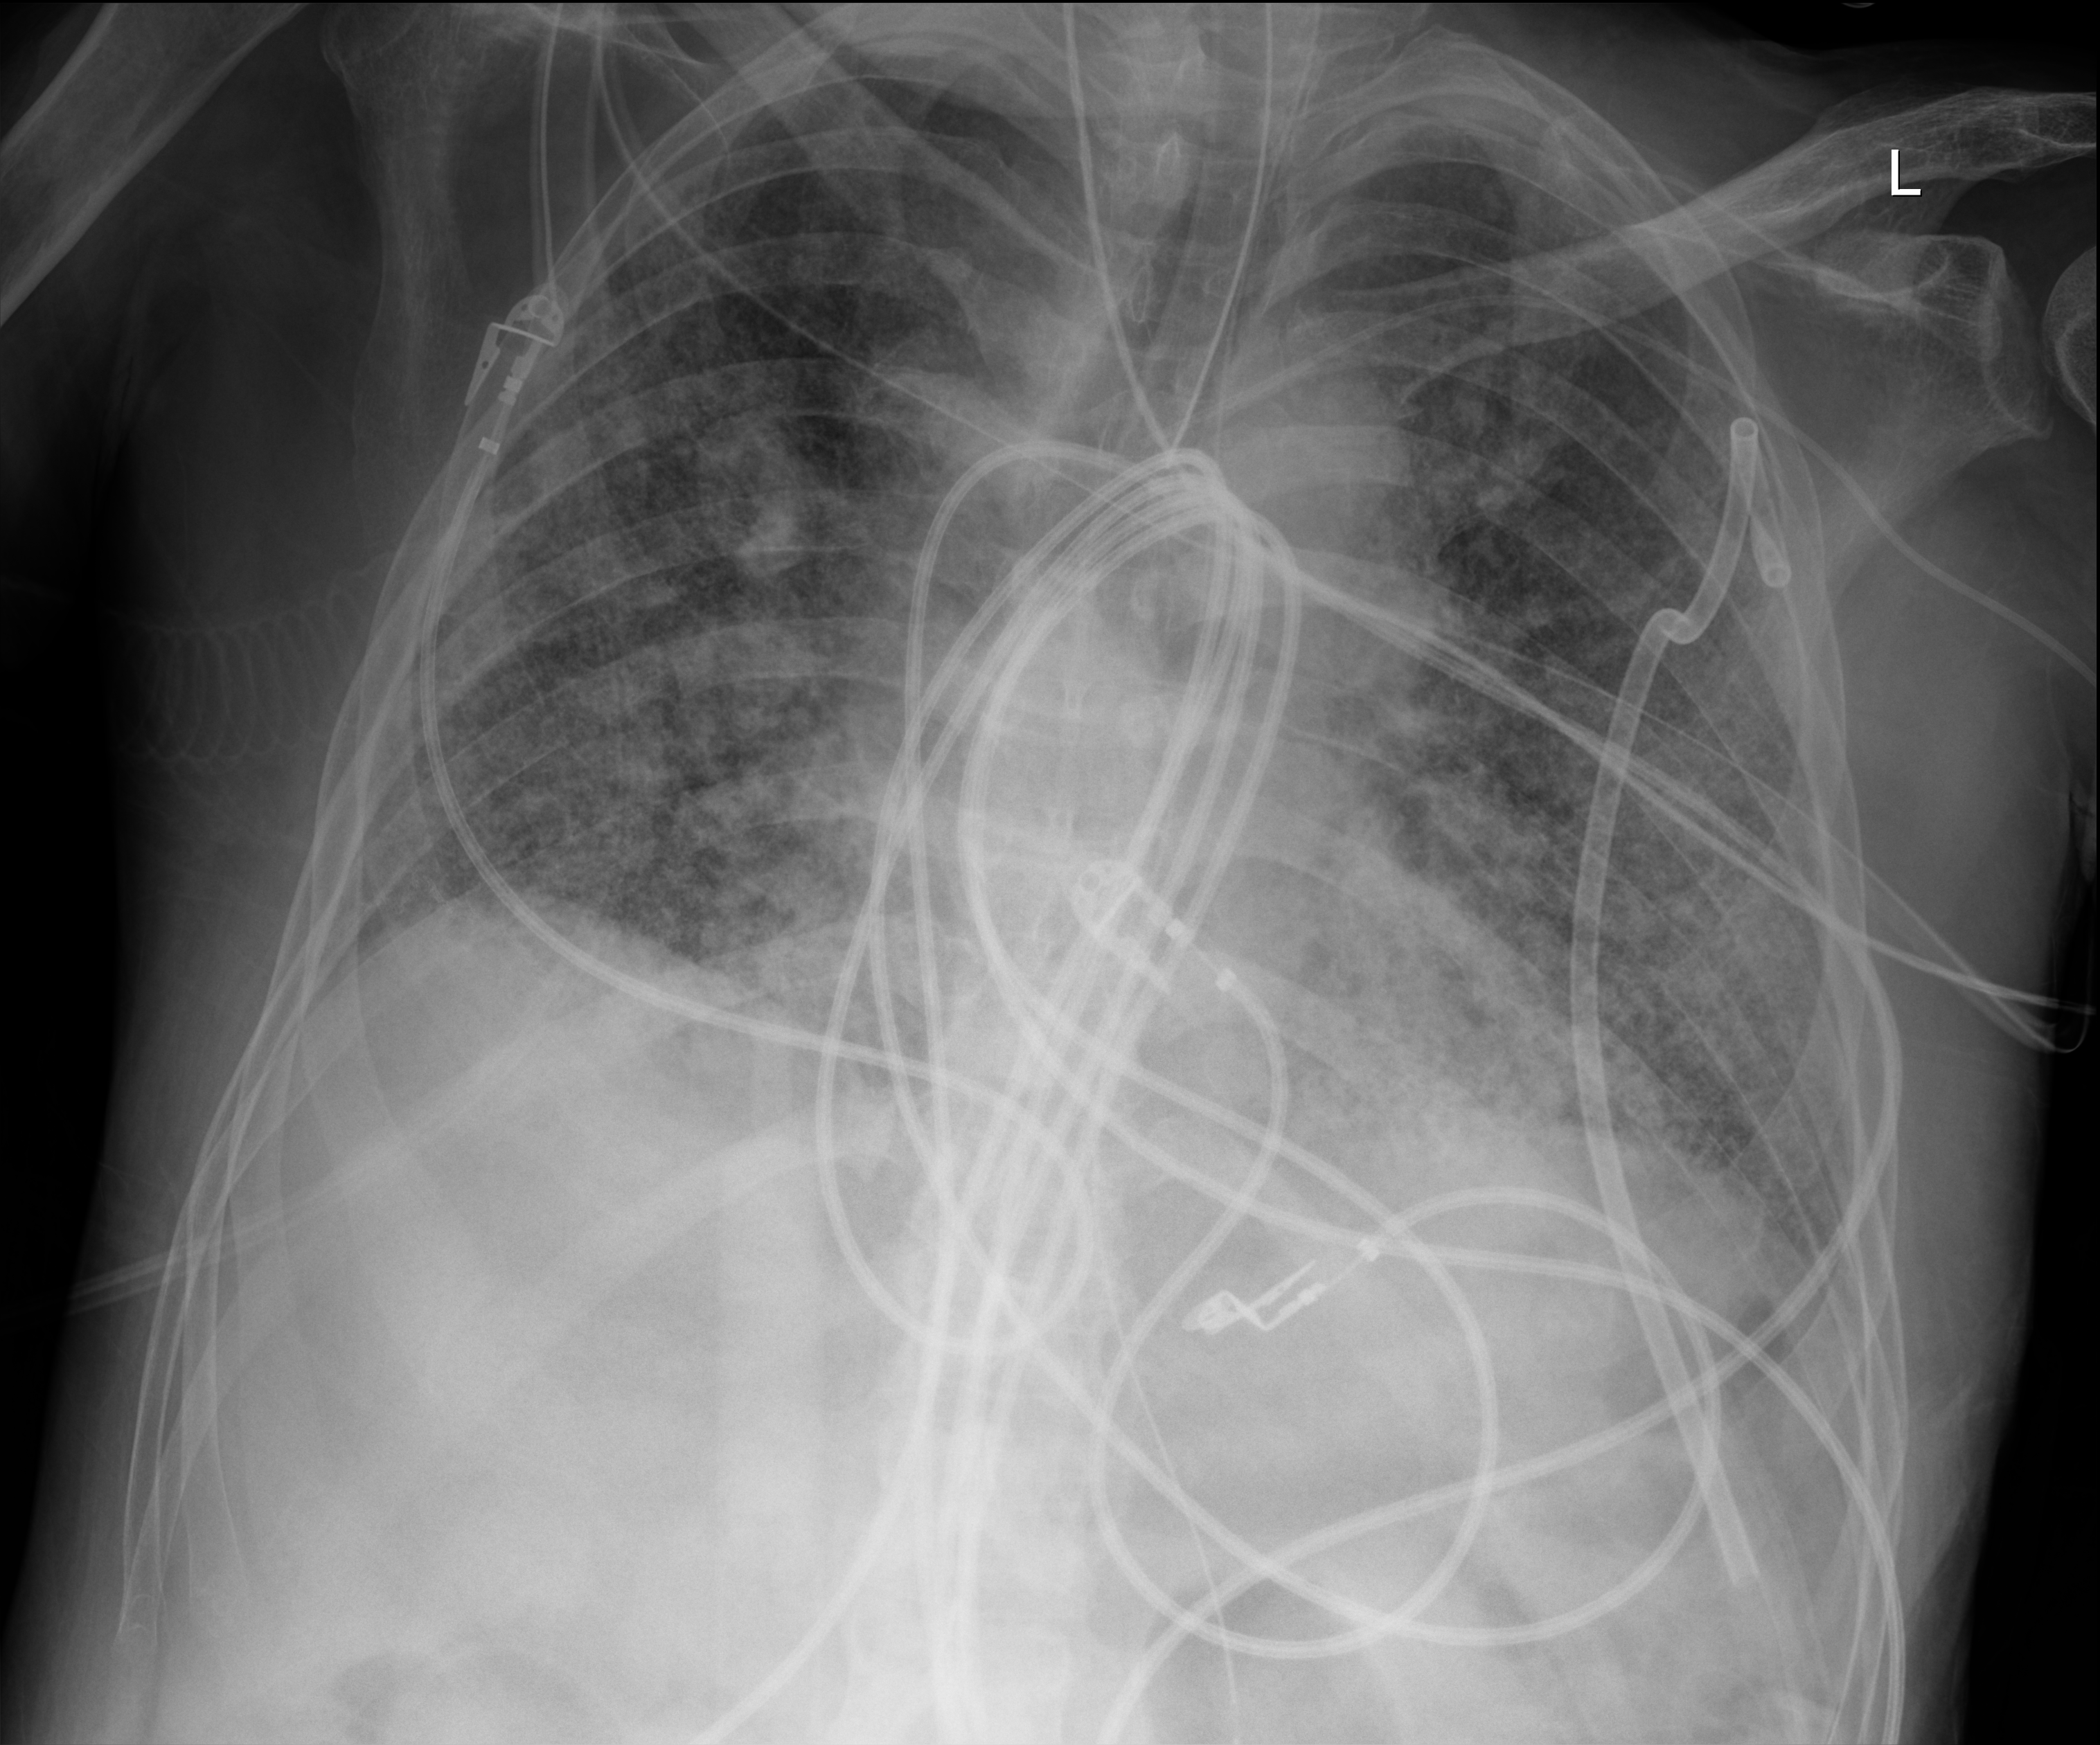
Portable chest radiograph, anteroposterior (AP) projection. Patient hospitalised with COVID-19; male, aged 60–74 years.
Admission-level facts for this patient (not findings on this image; timing relative to this image not recorded): admitted to intensive care during this hospital stay: yes; mechanically ventilated during this hospital stay: yes.